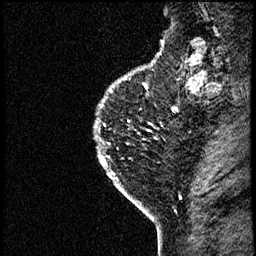
Breast MRI (dynamic contrast-enhanced), one sagittal slice; position 55 of 60 along the scan axis; dynamic contrast-enhanced study with each time point stored as its own series, time point 2 of 4 at this slice position (early post-contrast, ordered by acquisition time); 1.5 T; TE 4.2 ms, TR 17.6 ms; 256 × 256 image matrix, field of view 200 × 200 mm. Female patient, age 40 years. From the clinical record (not read from this slice): setting: breast cancer imaged before/during neoadjuvant chemotherapy; receptor status: HER2-positive.
Structures marked on this image (semi-automatically segmented with operator editing):
- analysis volume of interest (the breast-tissue region the enhancement analysis was run in; not a lesion): bounding box [x1, y1, x2, y2] px = [88, 55, 185, 206]
- tumour enhancement mask (voxels above the 100 % enhancement threshold inside the analysis volume of interest): [101, 160, 141, 206]